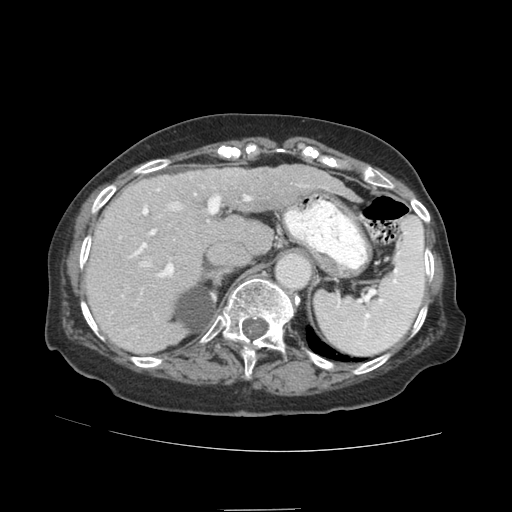
Contrast-enhanced abdominal CT (liver protocol), one axial slice. Reconstruction kernel STANDARD. 140 kVp. Soft-tissue window (W 400 / L 40 HU). 2.5 mm slice thickness. 512 × 512 image matrix, field of view 360 × 360 mm. From the clinical record (not read from this slice): diagnosis: hepatocellular carcinoma (patient treated with transarterial chemoembolisation; whether this scan precedes or follows treatment is not stated here); TNM stage (as recorded): Stage-II.
Structures marked on this image (semi-automatically segmented with operator editing):
- liver parenchyma outside the tumour (the mass and vessels are separate outlines, so this box may not span the whole liver): bounding box [x1, y1, x2, y2] px = [86, 164, 326, 352]
- liver vessels: [111, 174, 306, 344]